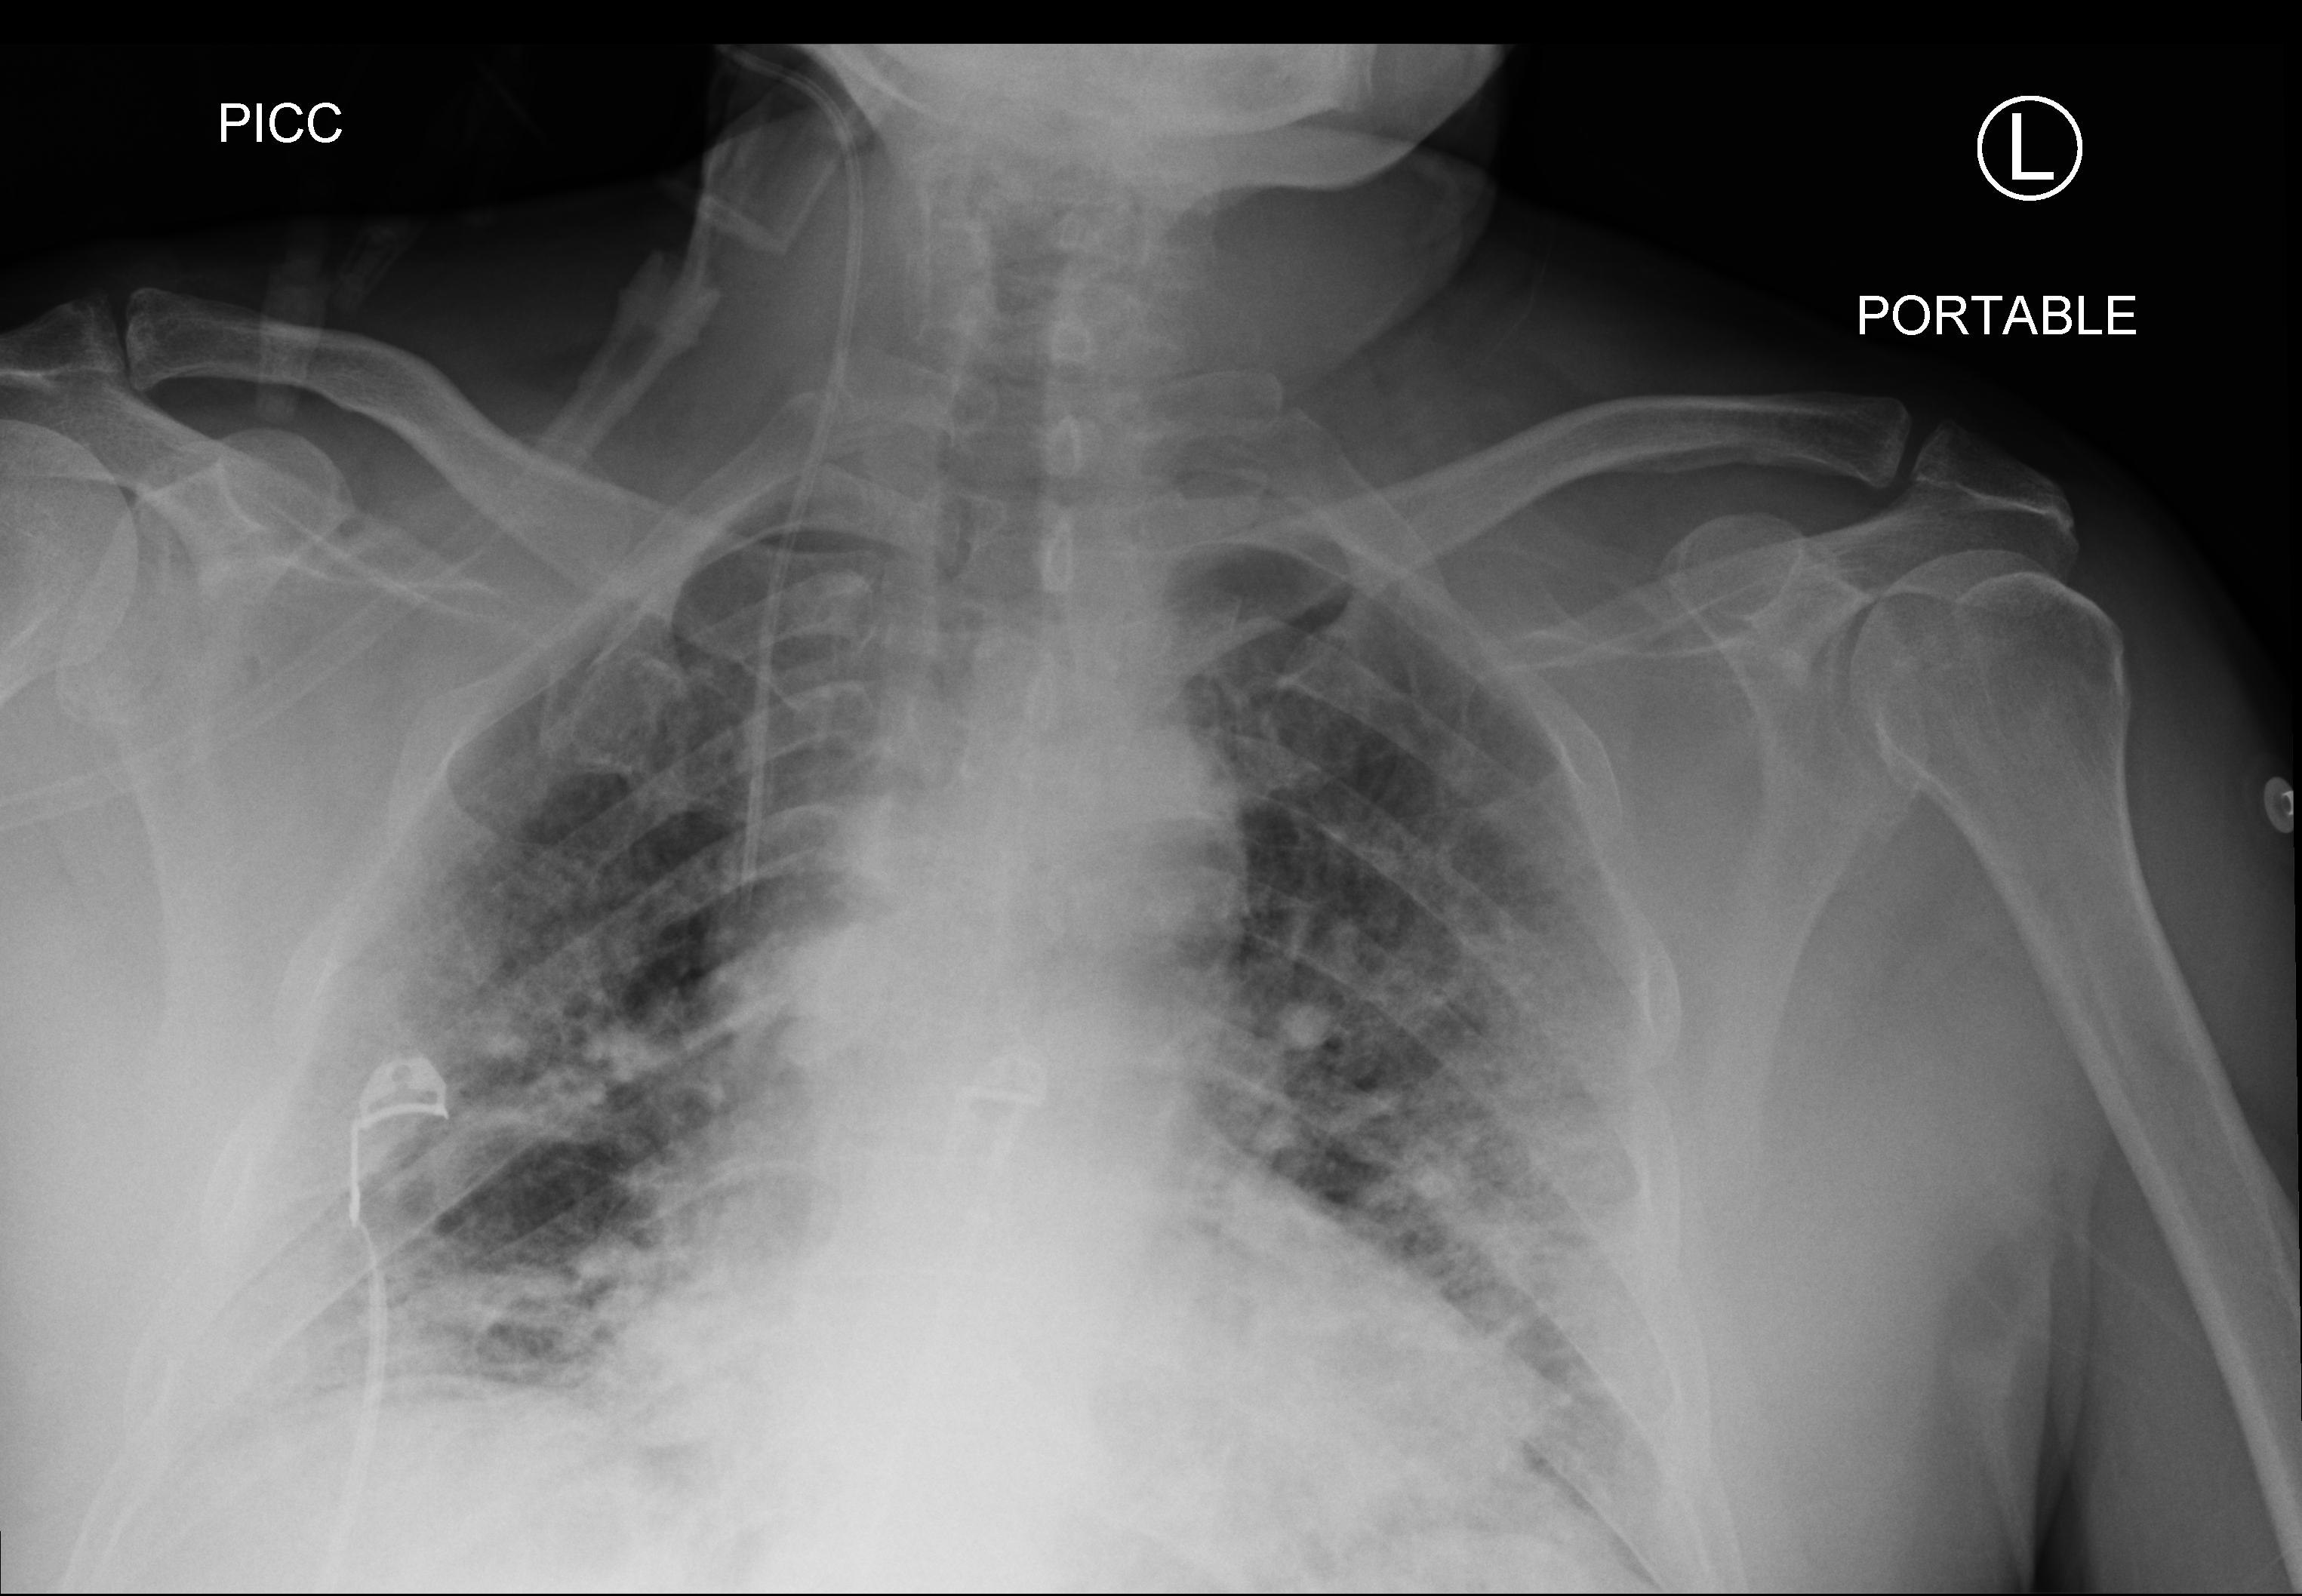
Chest X-ray (portable). Male patient hospitalised with COVID-19, age 60–74 years.
Hospital-stay facts (about this admission, not read from this image; timing relative to this image not recorded):
- smoking status (admission record): never
- mechanically ventilated during this hospital stay: yes
- admitted to intensive care during this hospital stay: yes